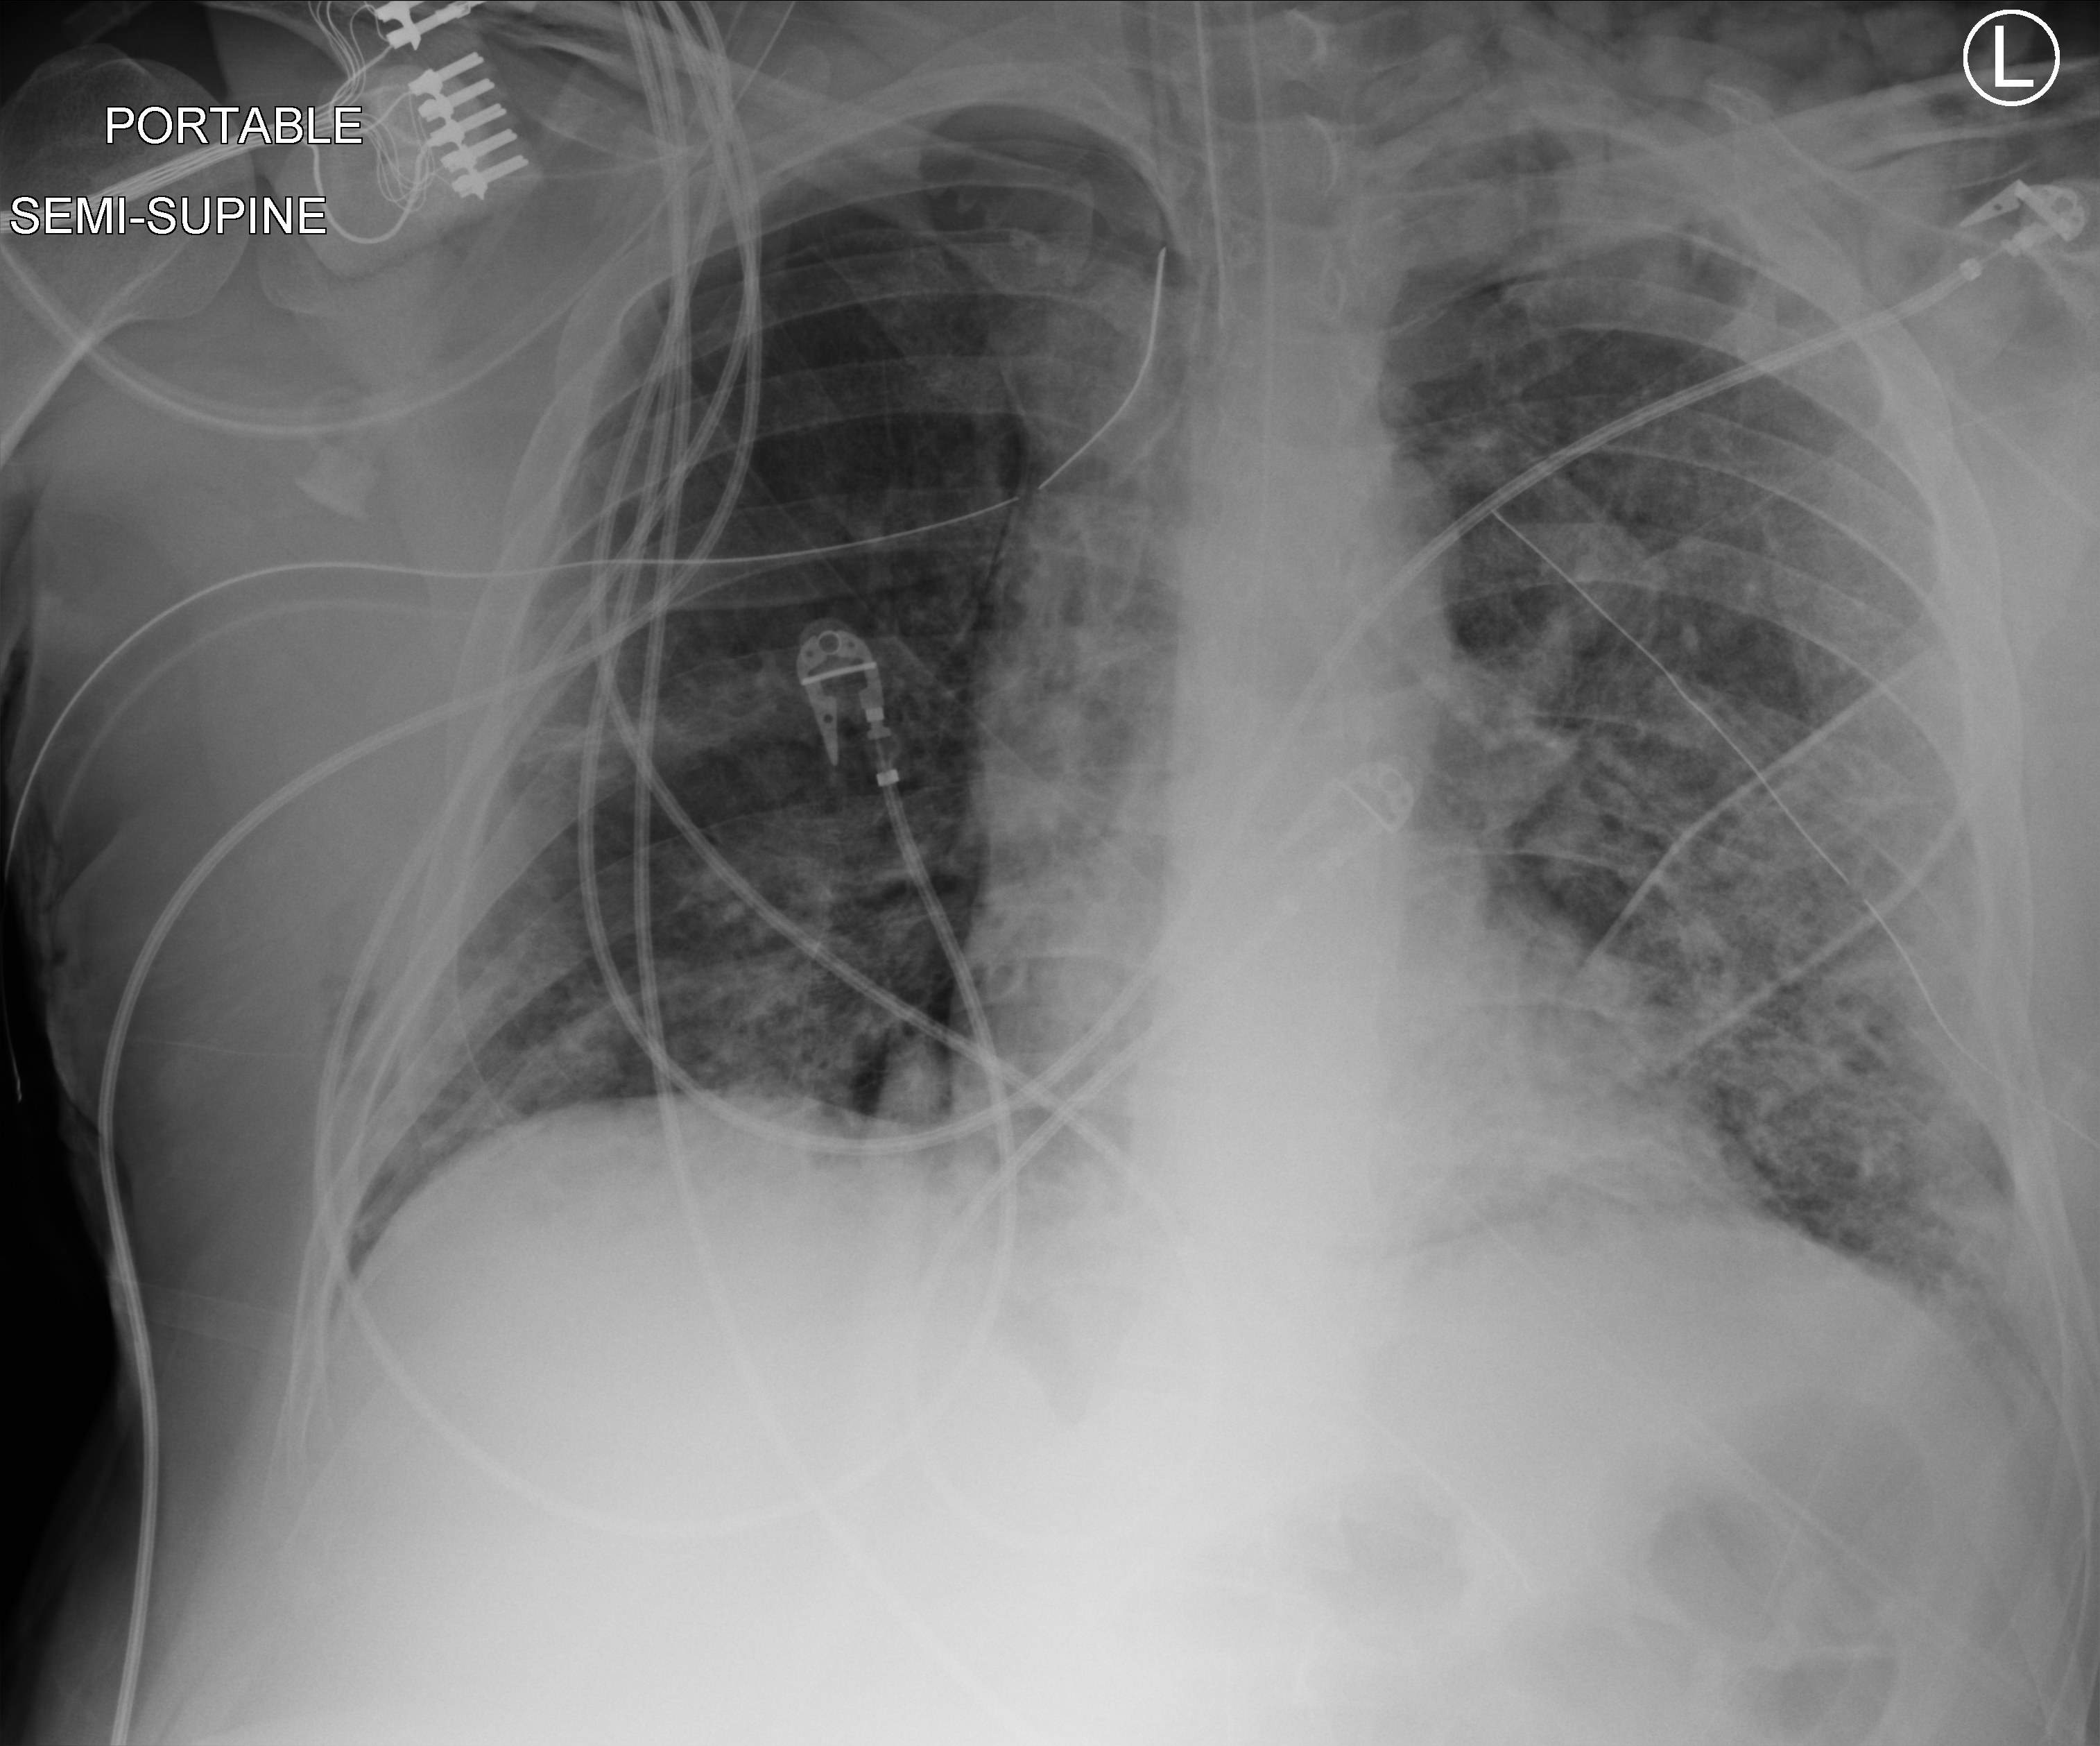
Bedside chest radiograph (computed radiography), anteroposterior (AP) projection. Patient hospitalised with COVID-19; male, aged 18–59 years.
Admission-level facts for this patient (not findings on this image; timing relative to this image not recorded): chronic kidney disease (admission record): no; admitted to intensive care during this hospital stay: yes; mechanically ventilated during this hospital stay: yes.